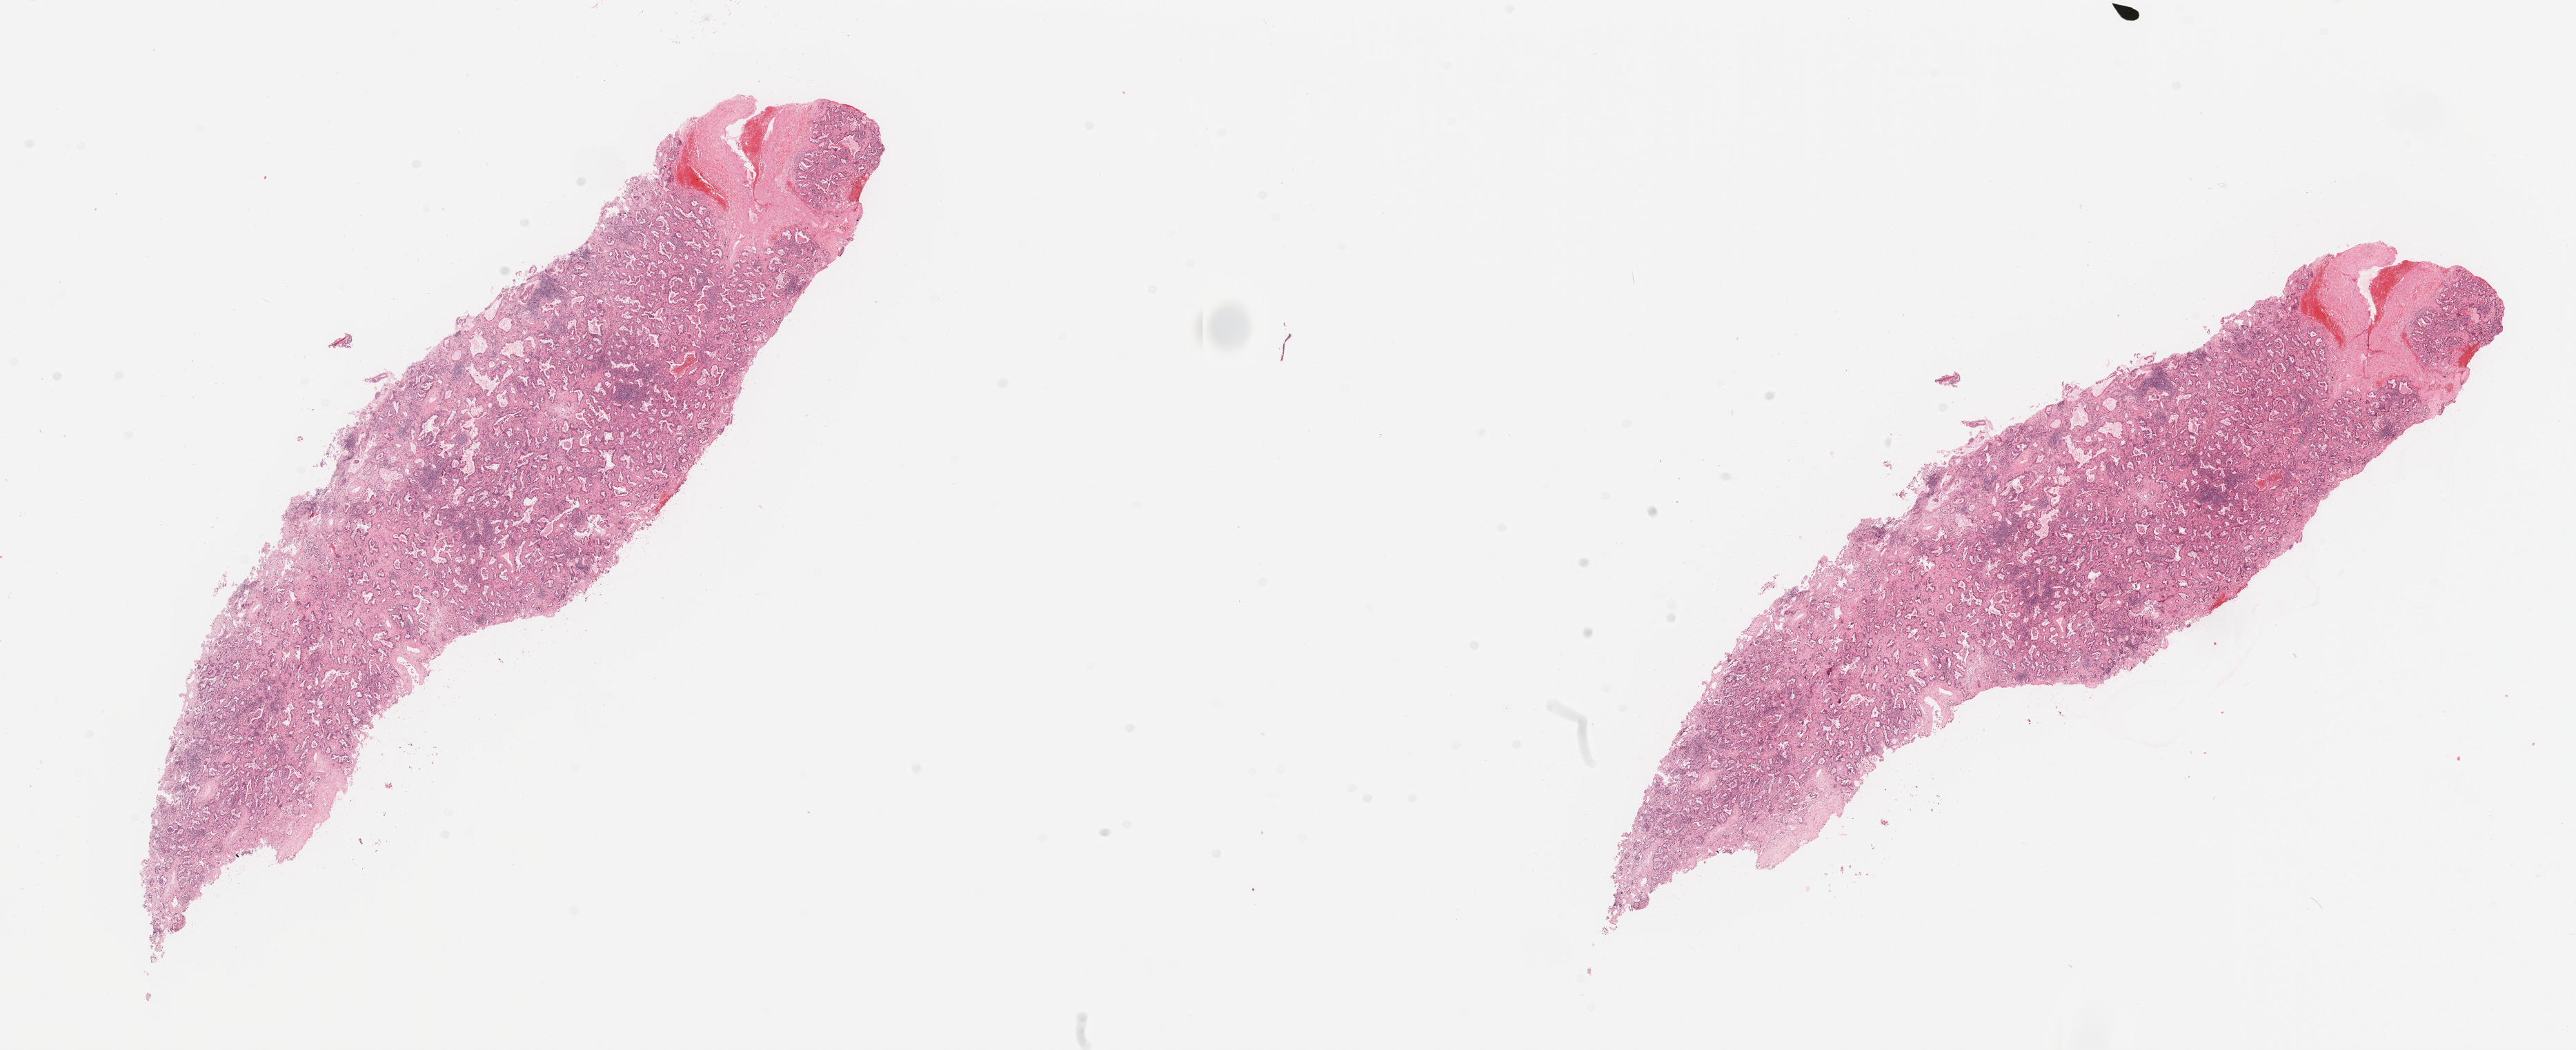
H&E-stained whole-slide image — a low-resolution overview of the entire scanned area, about 29.5 x 12.0 mm (slide scanned at 20x). Lung, tumour tissue. Patient: female, age 72 years. Histologic grade: G2 (moderately differentiated).
• diagnosis: Adenocarcinoma, NOS
• AJCC pathologic stage: IB